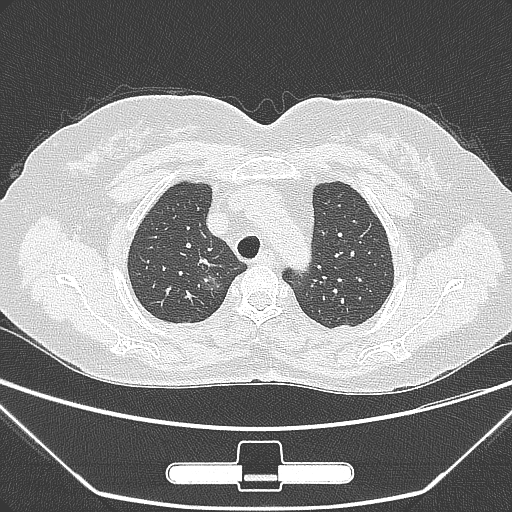
Chest CT, one axial slice; position 226 of 275 along the scan axis; lung window (W 1500 / L -600 HU); 1 mm slice thickness; 512 × 512 image matrix. Female patient, age 63 years. Case-level facts recorded for this patient, not image findings: clinical TNM (as recorded): T1a N0 M0; histopathological grade: G1.
Structures marked on this image (bounding box drawn by a radiologist):
- lung tumour (recorded histology: adenocarcinoma): bounding box (x1, y1, x2, y2) in pixels: (197, 269, 229, 303)